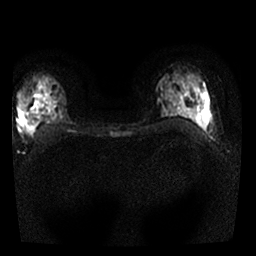
Breast MRI, one axial slice; position 15 of 25 along the scan axis; diffusion-weighted series; image 2 of 4 stored at this slice position (different b-values; order by instance number); 1.5 T; 4 mm slice thickness; 256 × 256 image matrix, field of view 300 × 300 mm. Female patient.
Structures marked on this image (expert manual segmentation):
- tumour on diffusion-weighted imaging: bounding box (x1, y1, x2, y2) in pixels: (19, 110, 35, 127)